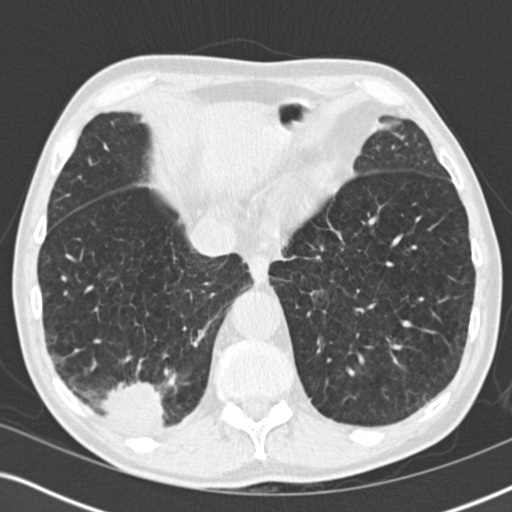
Chest CT (low-dose screening protocol), one axial image; baseline annual screen; lung window (W 1500 / L -600 HU); standard (soft-tissue) reconstruction kernel (B30f); slice 141 of 196 in the series. Male participant, aged 64 years at enrolment. Former smoker at enrolment.
Expert-annotated lung lesion, bounding box (x1, y1, x2, y2) in pixels: (80, 366, 179, 449). The screening reader recorded 3 non-calcified nodules or masses ≥4 mm on this exam (lingula, lingula, right lower lobe); which of them this box marks is not recorded. Official screen result: positive, change unspecified: nodule(s) >= 4 mm or enlarging nodule(s), mass(es), or other non-specific abnormalities suspicious for lung cancer. Participant outcome: lung cancer diagnosed 27 days after this screen — squamous cell carcinoma, NOS, right lower lobe, moderately differentiated (G2), stage IV (AJCC 6th edition), 40 mm at pathology.